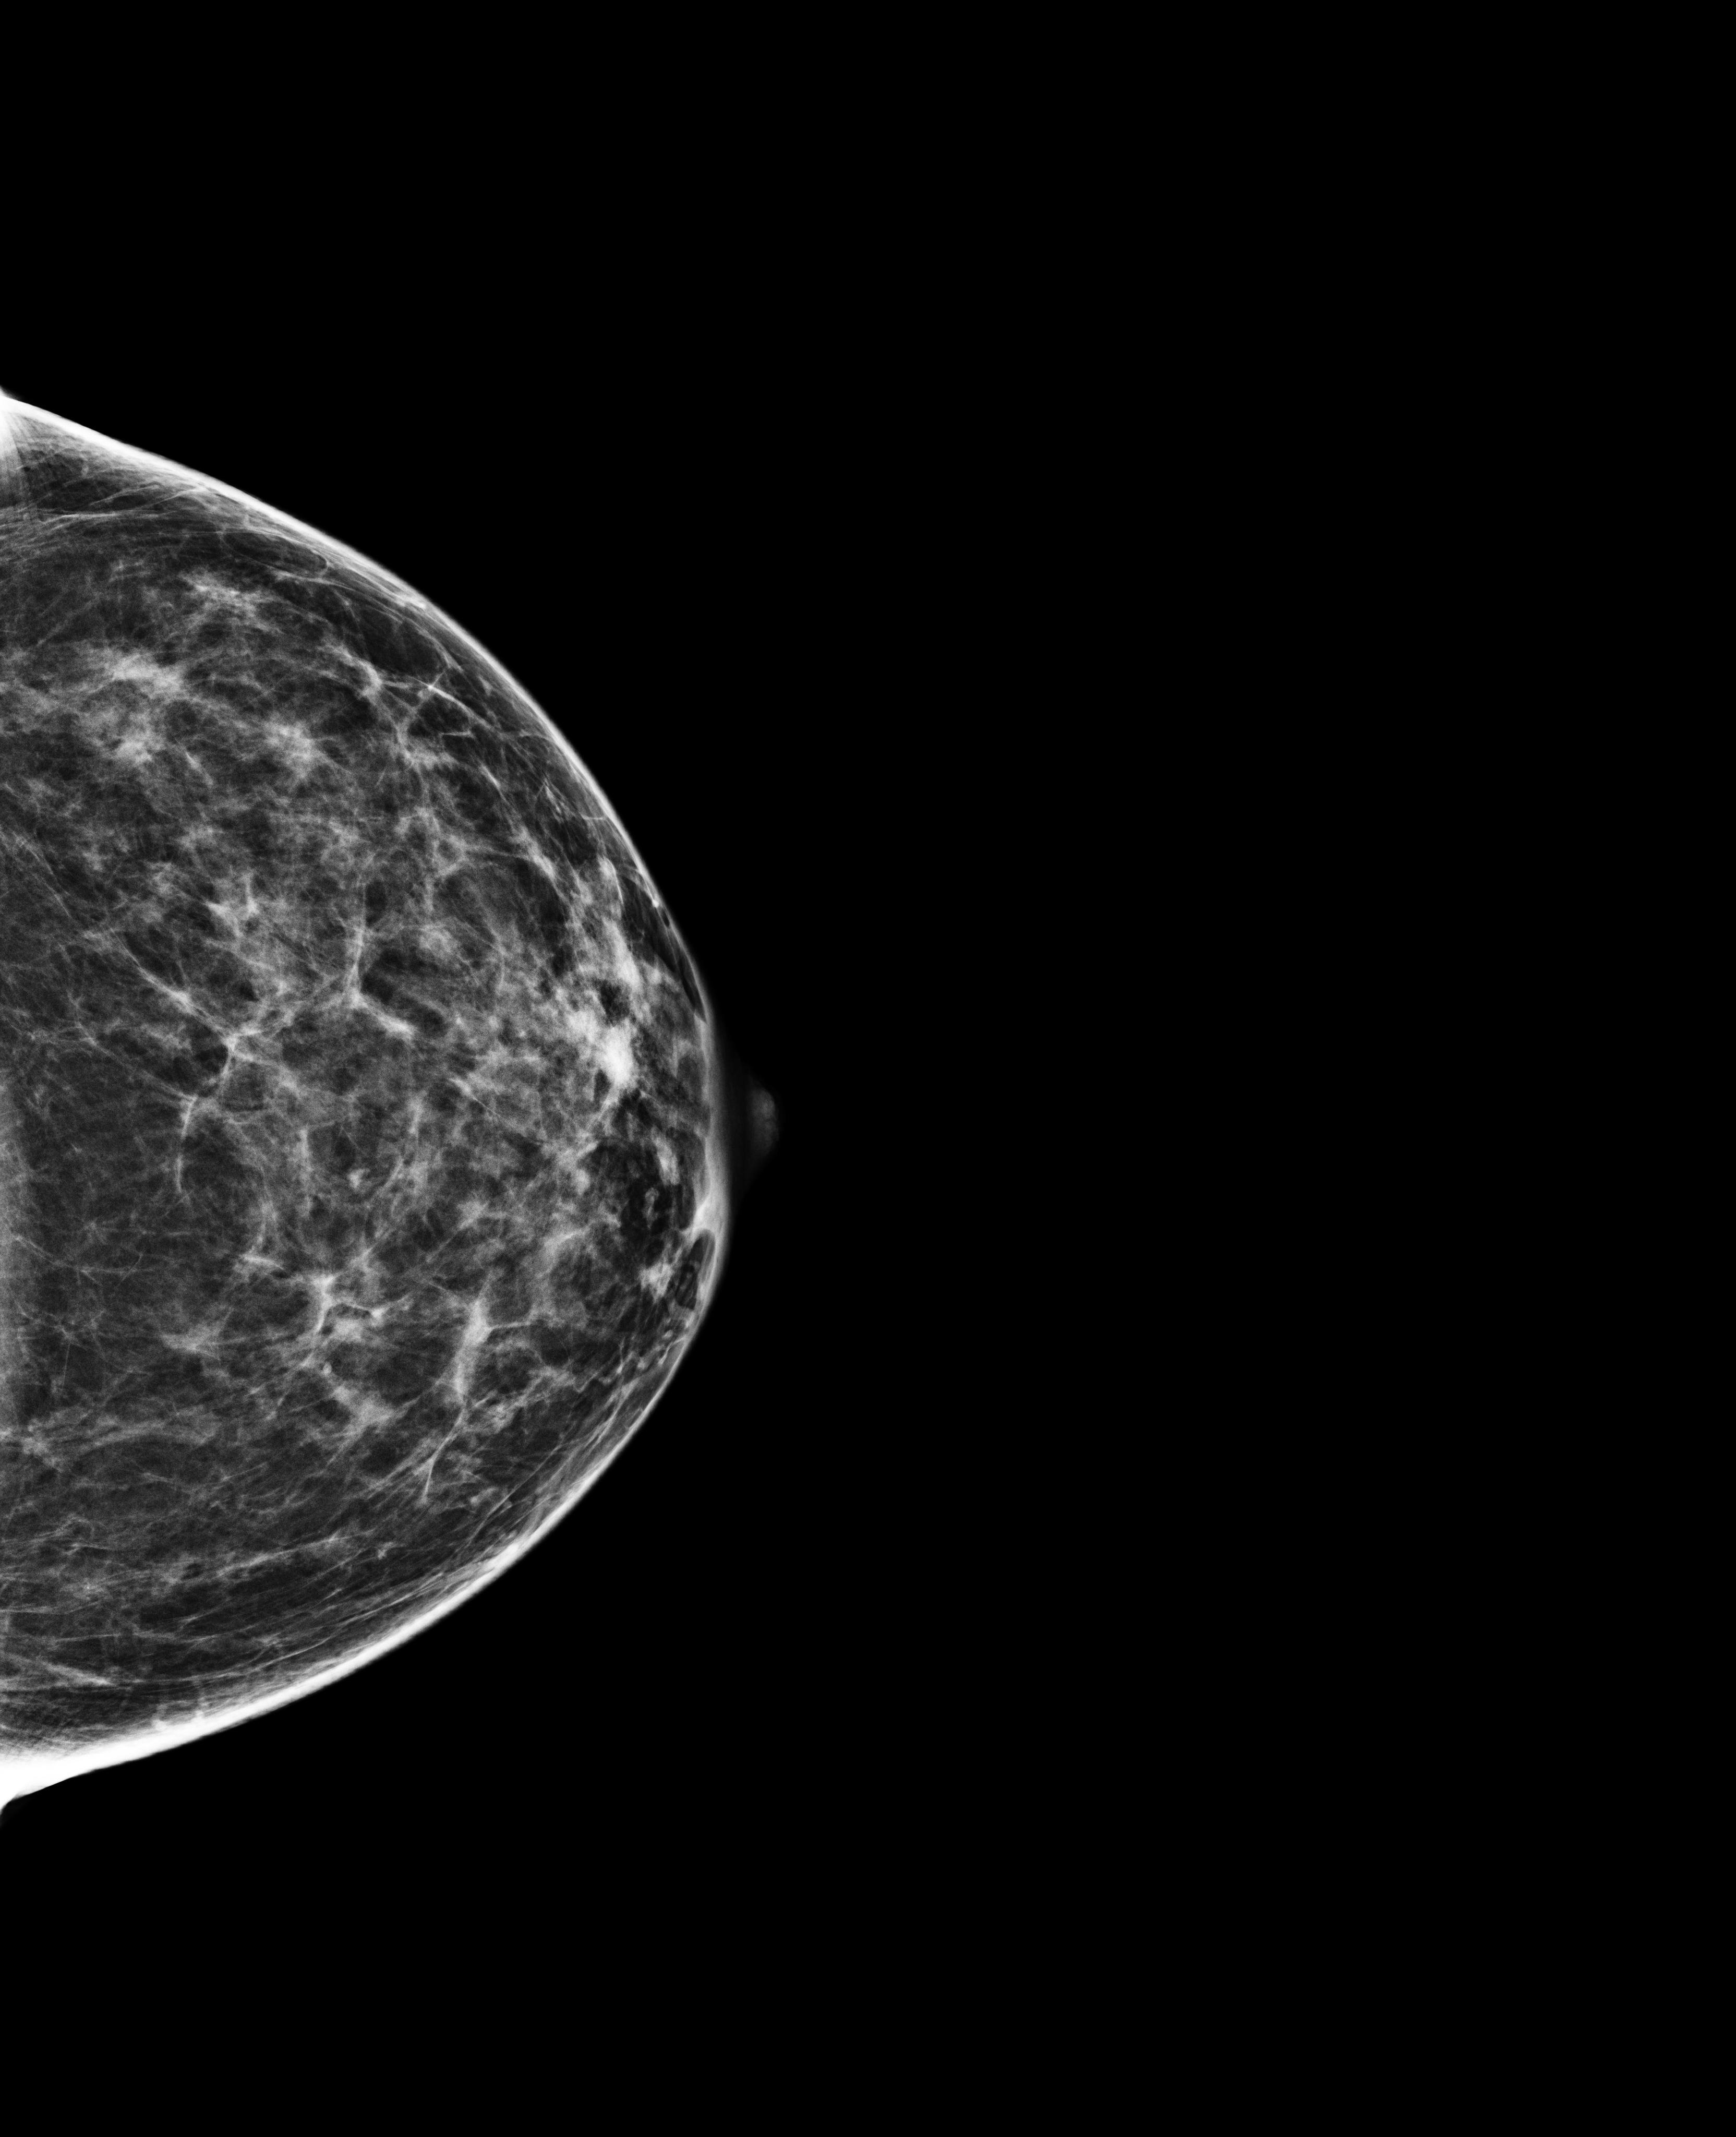
Full-field digital mammogram (FFDM), left breast, CC view, screening examination. Female patient, age 48 years.
- breast density at the screening exam (both breasts): scattered fibroglandular densities (BI-RADS density category b)
- final BI-RADS assessment for this screening round (tomosynthesis exam, both breasts): category 1
- recall: no recall after this screen